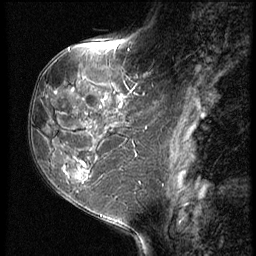
Breast MRI (dynamic contrast-enhanced), one sagittal slice; position 23 of 62 along the scan axis; 3 images stored at this slice position (order not interpretable as contrast timing); 1.5 T; TE 4.2 ms, TR 9 ms; 2.5 mm slice thickness; 256 × 256 image matrix. Female patient, age 50 years. Case-level facts recorded for this patient, not image findings: setting: breast cancer imaged before/during neoadjuvant chemotherapy; receptor status: HR-positive, HER2-negative.
Annotated regions visible in this slice (semi-automatically segmented with operator editing):
- analysis volume of interest (the breast-tissue region the enhancement analysis was run in; not a lesion): box from (x=32, y=91) to (x=118, y=209) px
- tumour enhancement mask (voxels above the 140 % enhancement threshold inside the analysis volume of interest): (x=79, y=160)–(x=88, y=174)